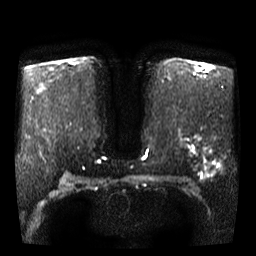
Breast MRI, one axial slice; slice 25 of 46 in the series (ordered by position); diffusion-weighted series; image 2 of 4 stored at this slice position (different b-values; order by instance number); 3 T; 5 mm slice thickness; 256 × 256 image matrix, field of view 340 × 340 mm. Female patient.
Structures marked on this image (expert manual segmentation):
- tumour on diffusion-weighted imaging: bounding box [x1, y1, x2, y2] px = [200, 158, 204, 161]